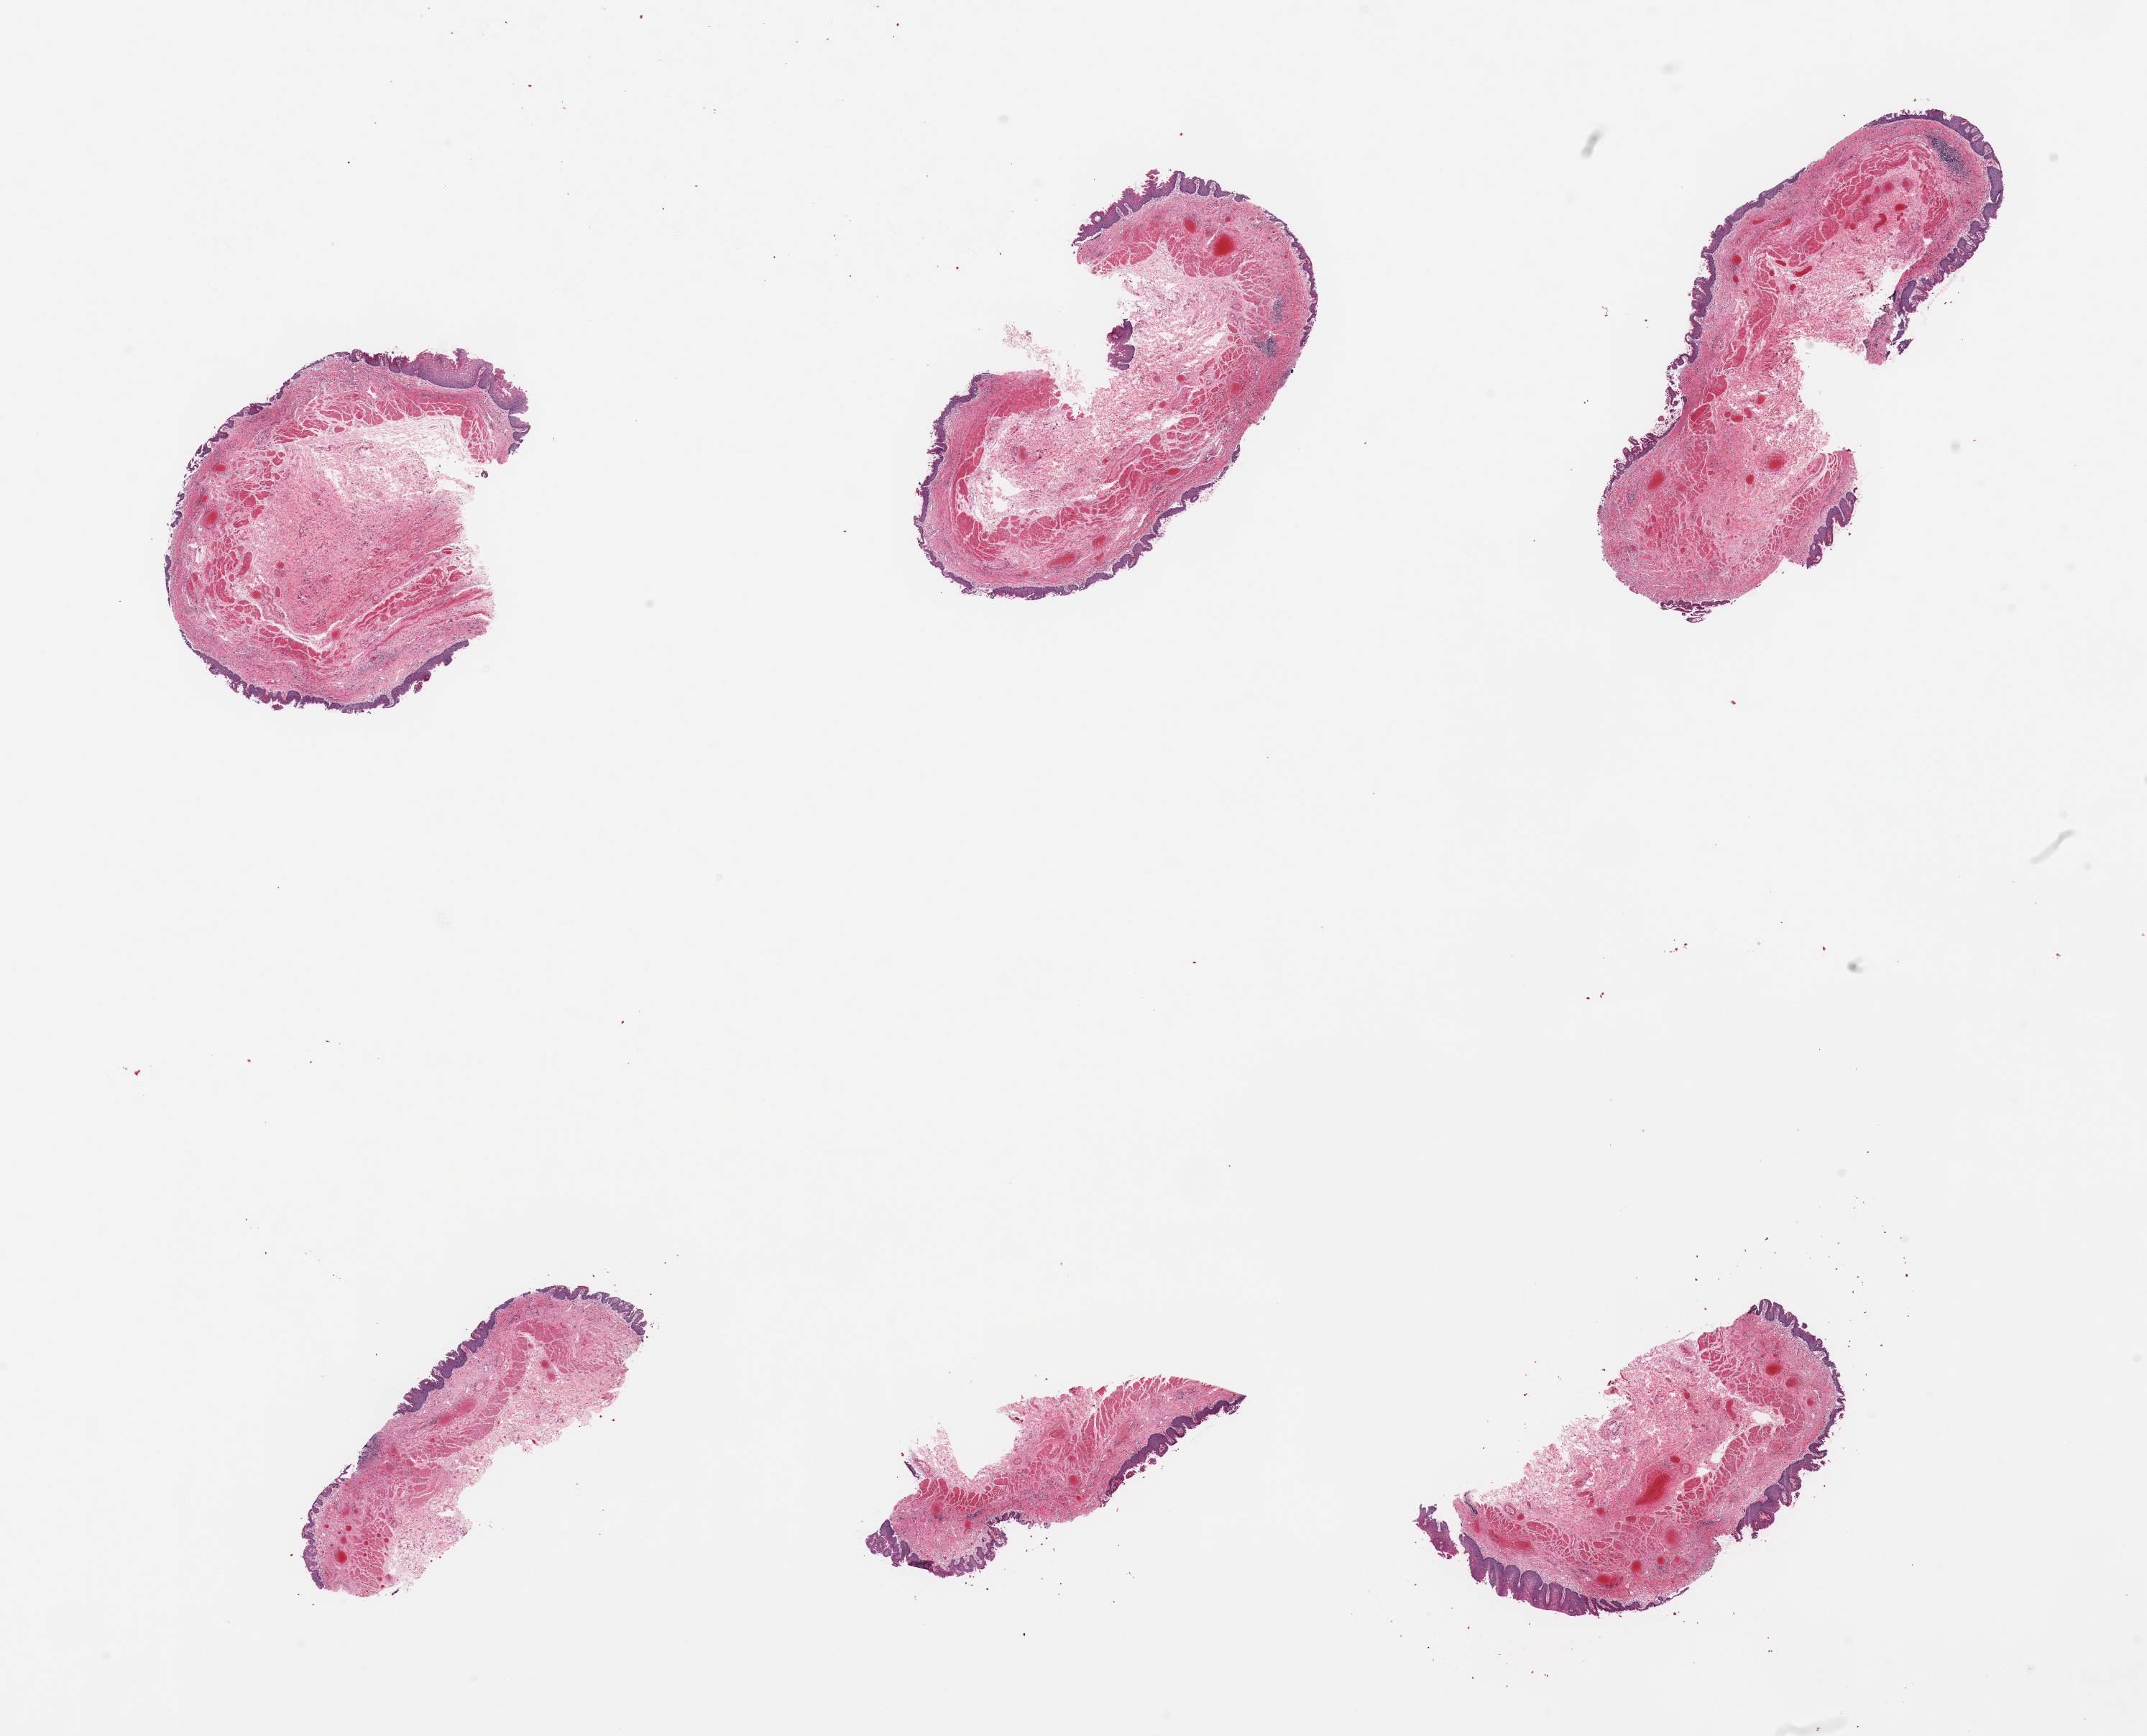
Digitized haematoxylin and eosin-stained section — low-resolution overview of the scanned area, about 23.6 x 19.1 mm (acquisition: 20x scan); PAXgene-fixed, paraffin-embedded tissue; target tissue: esophageal mucous membrane; tissue donor sample.
Pathologist's review note for this sample: 6 pieces; chronic inflammation; considerable epithelial sloughing.